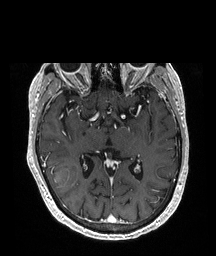
Brain MRI from a brain-tumour surgery series, one axial slice. Slice 117 of 208 in the series (ordered by position). T1-weighted post-contrast. 1 mm slice thickness. 216 × 256 image matrix. From the clinical record (not read from this slice): histopathology: Glioblastoma; WHO grade: 4; IDH mutation: no.
Structures marked on this image (outlined manually by an expert reader):
- tumour: bounding box [x1, y1, x2, y2] px = [46, 157, 77, 190]